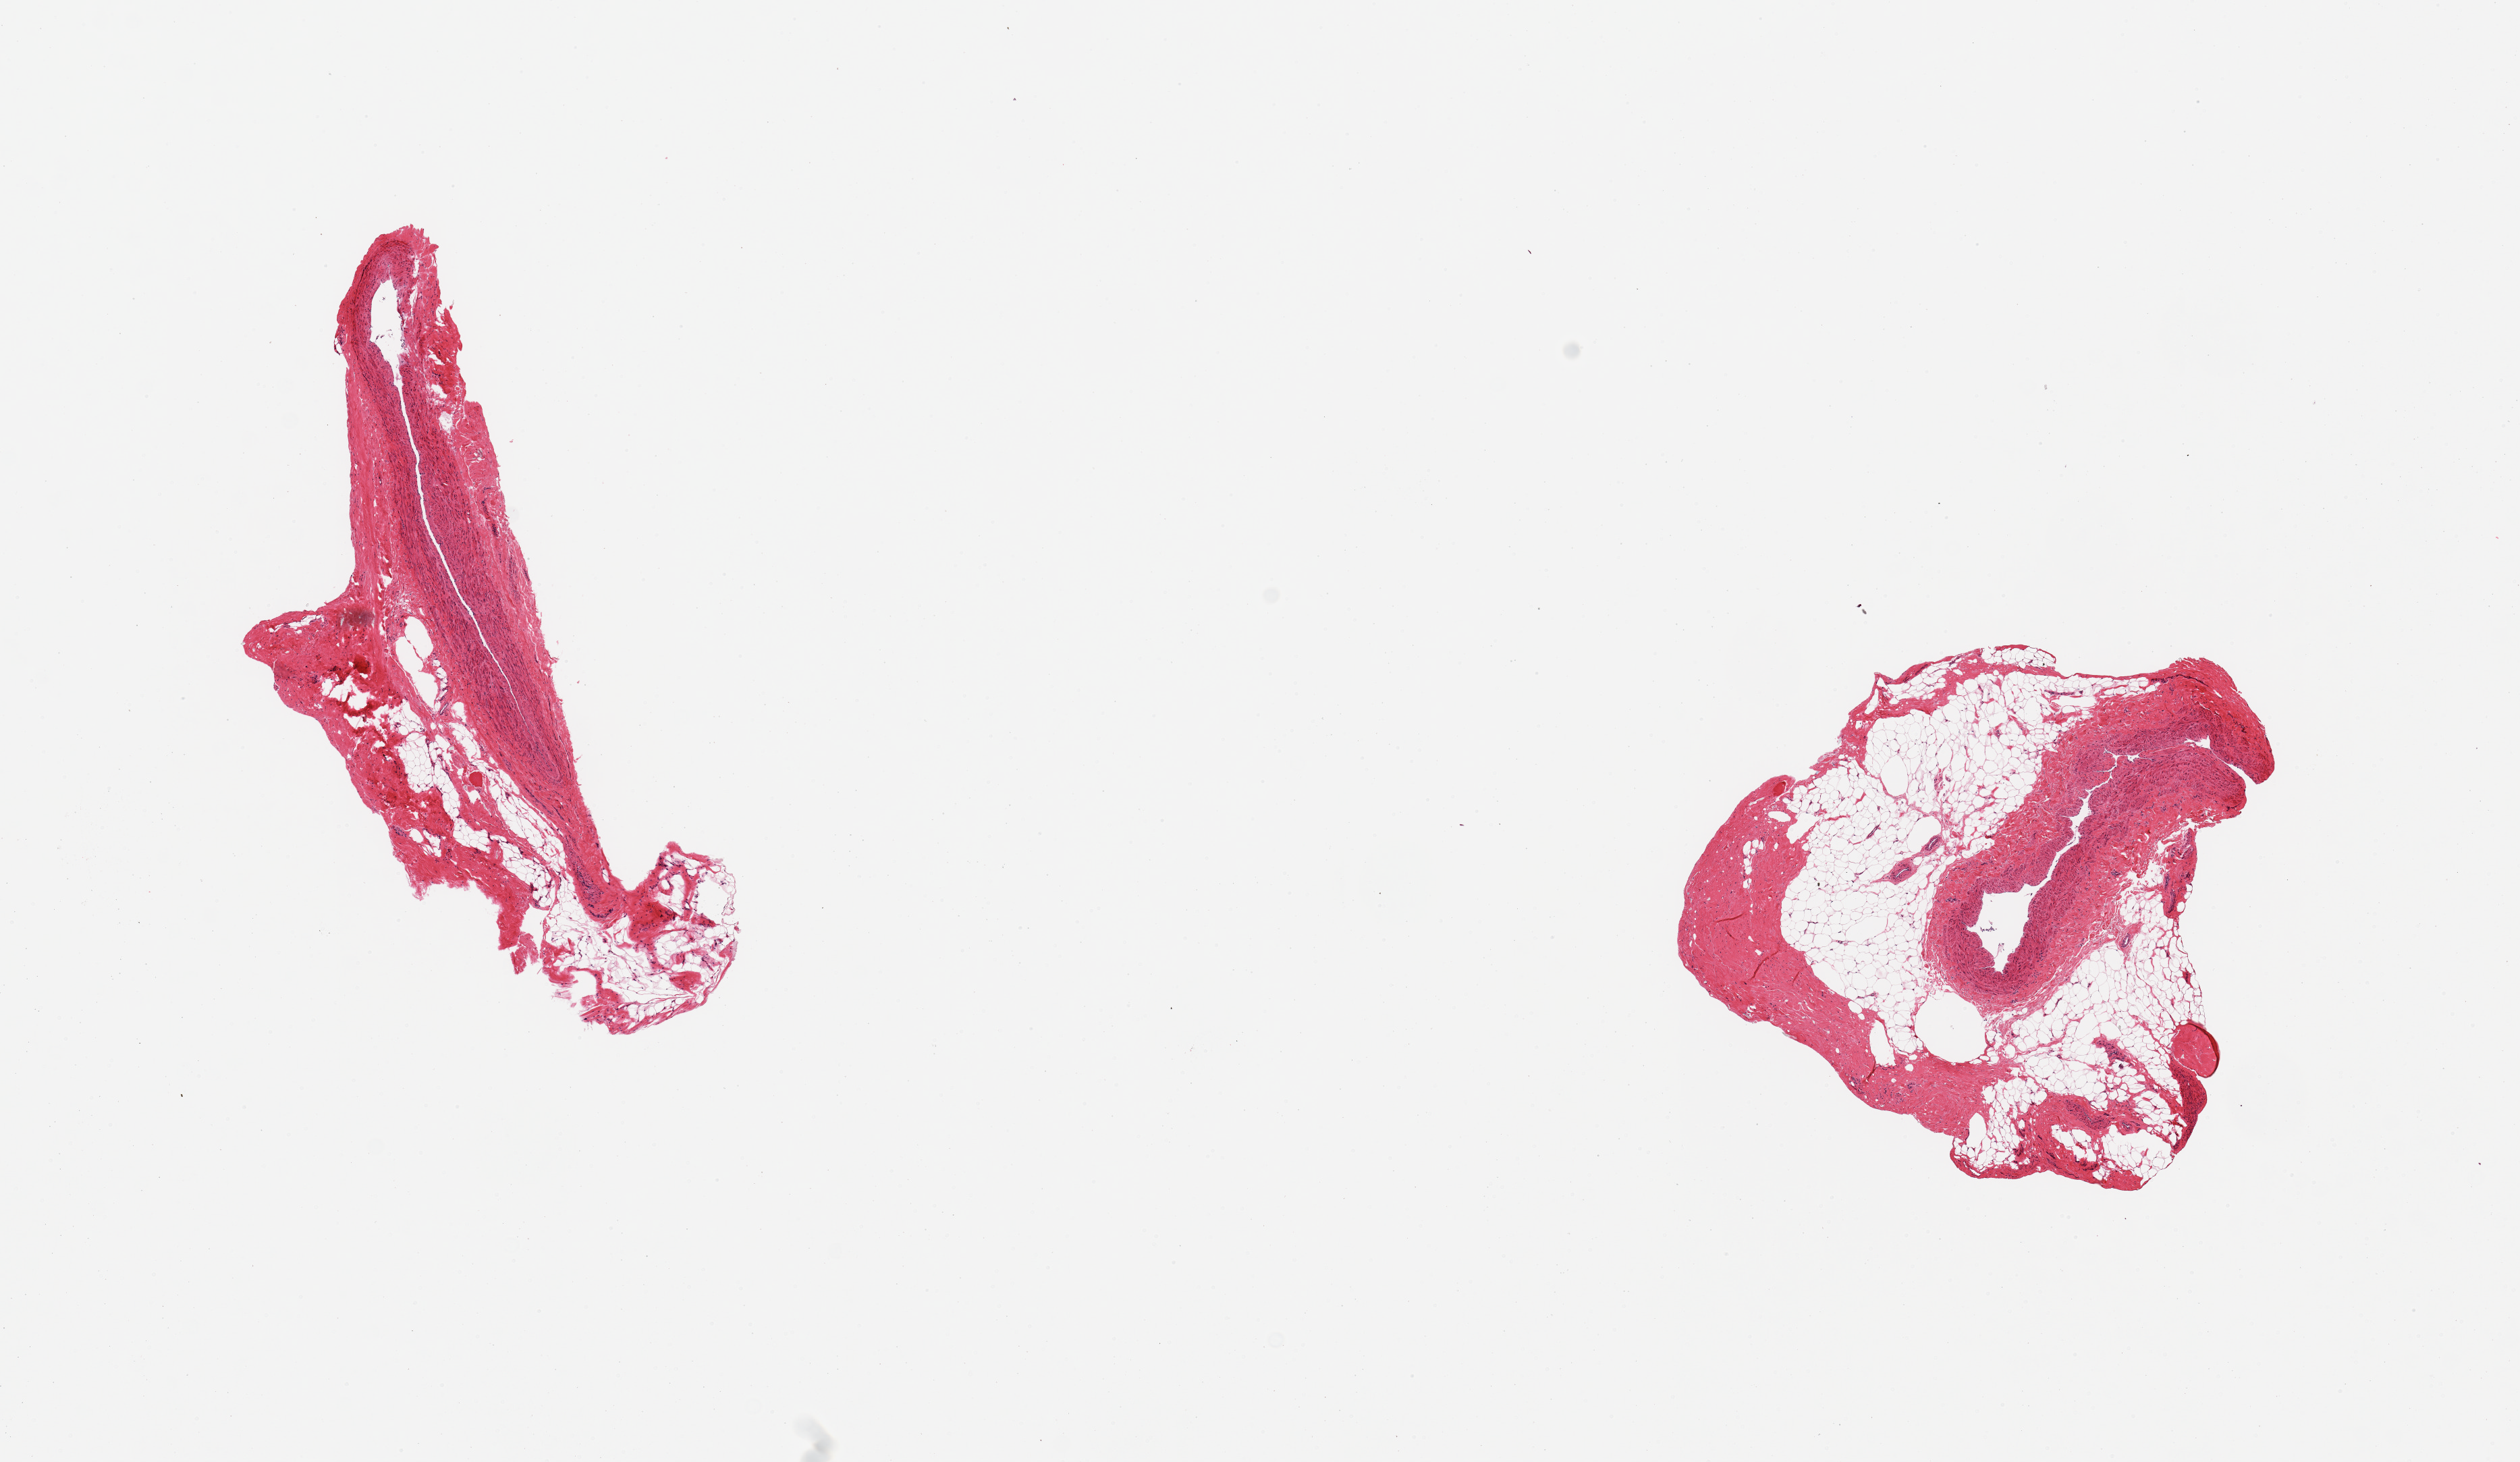
Digitized hematoxylin and eosin (H&E)-stained section, whole scanned area (about 14.8 x 8.6 mm, slide scanned at 20x) shown as a low-resolution overview. PAXgene-fixed, paraffin-embedded tissue. Section of tibial artery (target tissue). Donor tissue sample. Donor: female.
Pathologist's review note for this sample: 2 pieces; external fat occupies 70% & 50%.